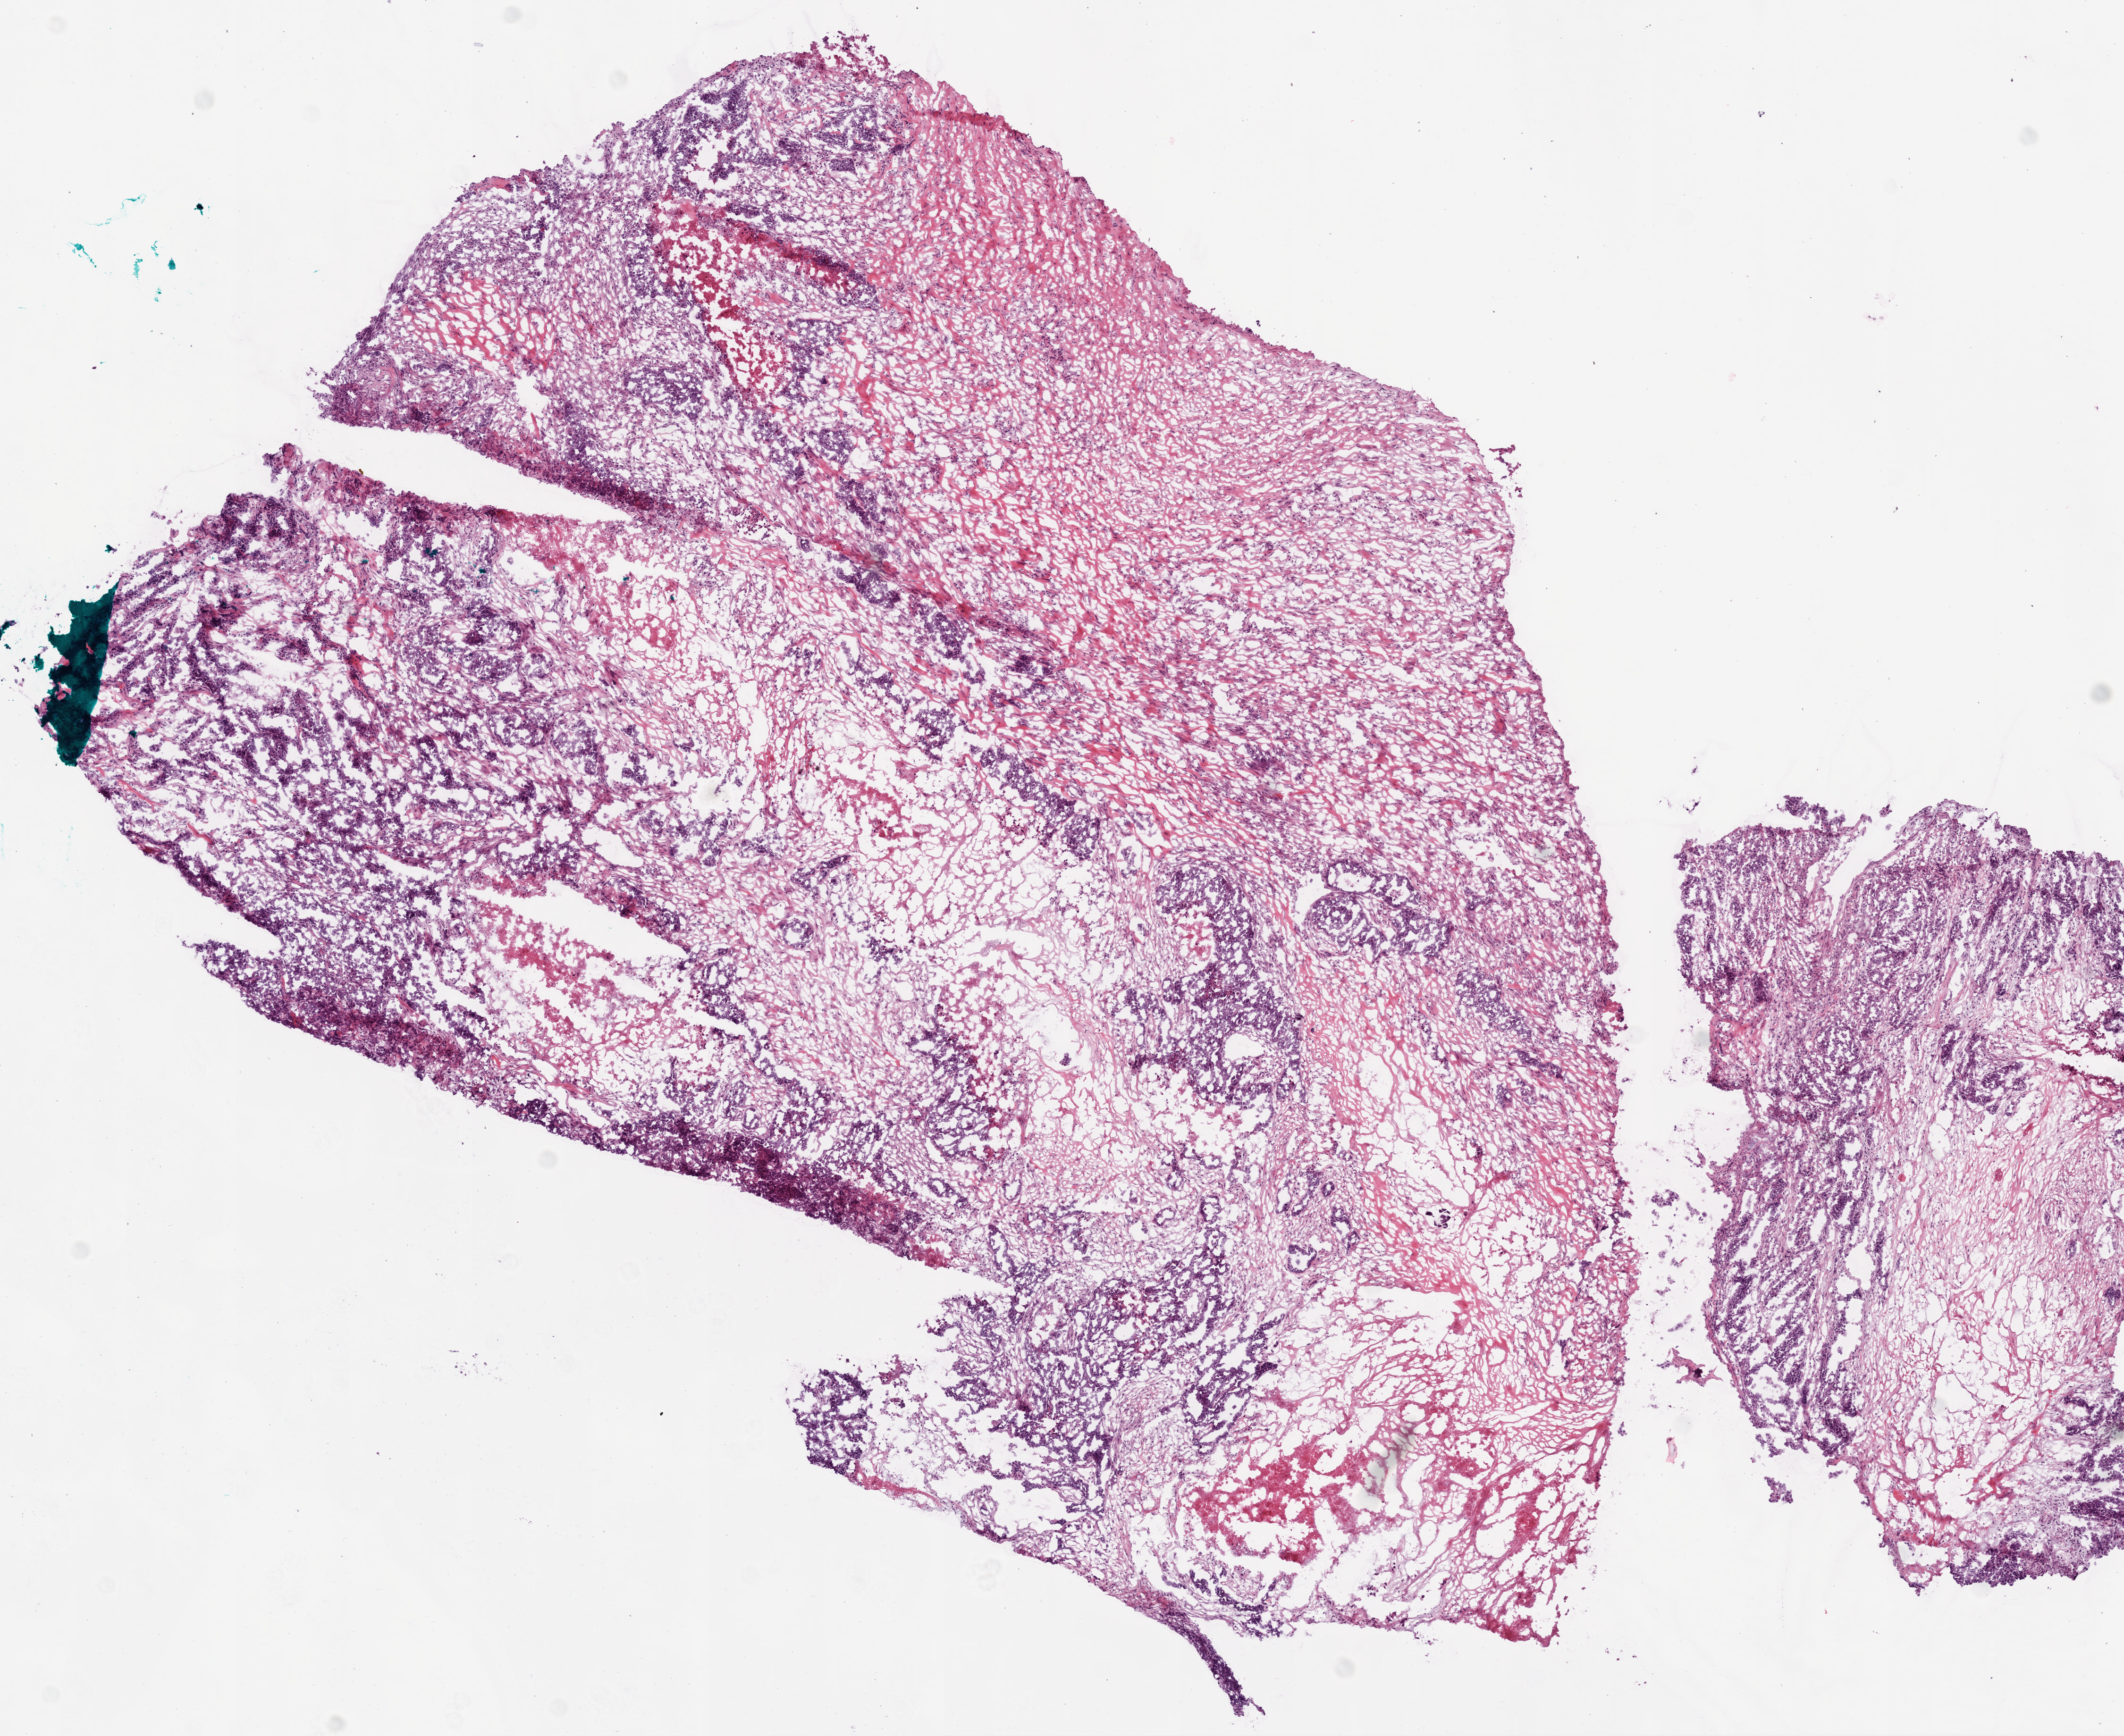
H&E-stained whole-slide image, a low-resolution overview of the entire scanned area, about 9.0 x 7.4 mm; frozen section from the bottom of the tissue portion; primary tumour sample from the ovary. Patient: female, age at initial diagnosis 68 years. Histologic grade: G3 (poorly differentiated). Pathologist review of this section (percent, as recorded): tumour cells 40%, tumour nuclei 70%, normal cells 45%, stromal cells 0%, necrosis 15%.
Histologic diagnosis: Serous cystadenocarcinoma, NOS. FIGO stage: IIIC.